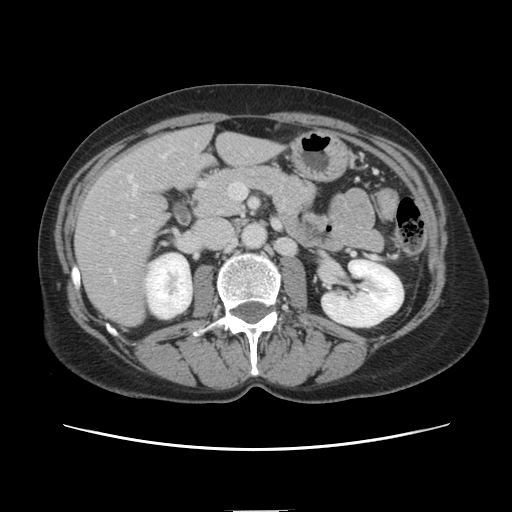
Contrast-enhanced abdominal CT, one axial slice. Slice 54 of 141 in the series (ordered by position). Intravenous contrast given. Soft-tissue window (W 400 / L 40 HU). 2.5 mm slice thickness. 512 × 512 image matrix. Female patient, age 63 years. From the clinical record (not read from this slice): diagnosis: colorectal cancer liver metastases, imaged before liver resection; multiple liver metastases: yes; largest metastasis: 3.2 cm; disease in both lobes: yes.
Outlined on this slice (manually delineated by an expert):
- hepatic veins: box from (x=112, y=176) to (x=137, y=233) px
- liver: (x=76, y=127)–(x=279, y=327)
- planned liver remnant (the part of the liver to remain after resection): (x=177, y=128)–(x=279, y=180)
- portal vein (with intrahepatic branches): (x=131, y=179)–(x=136, y=193)